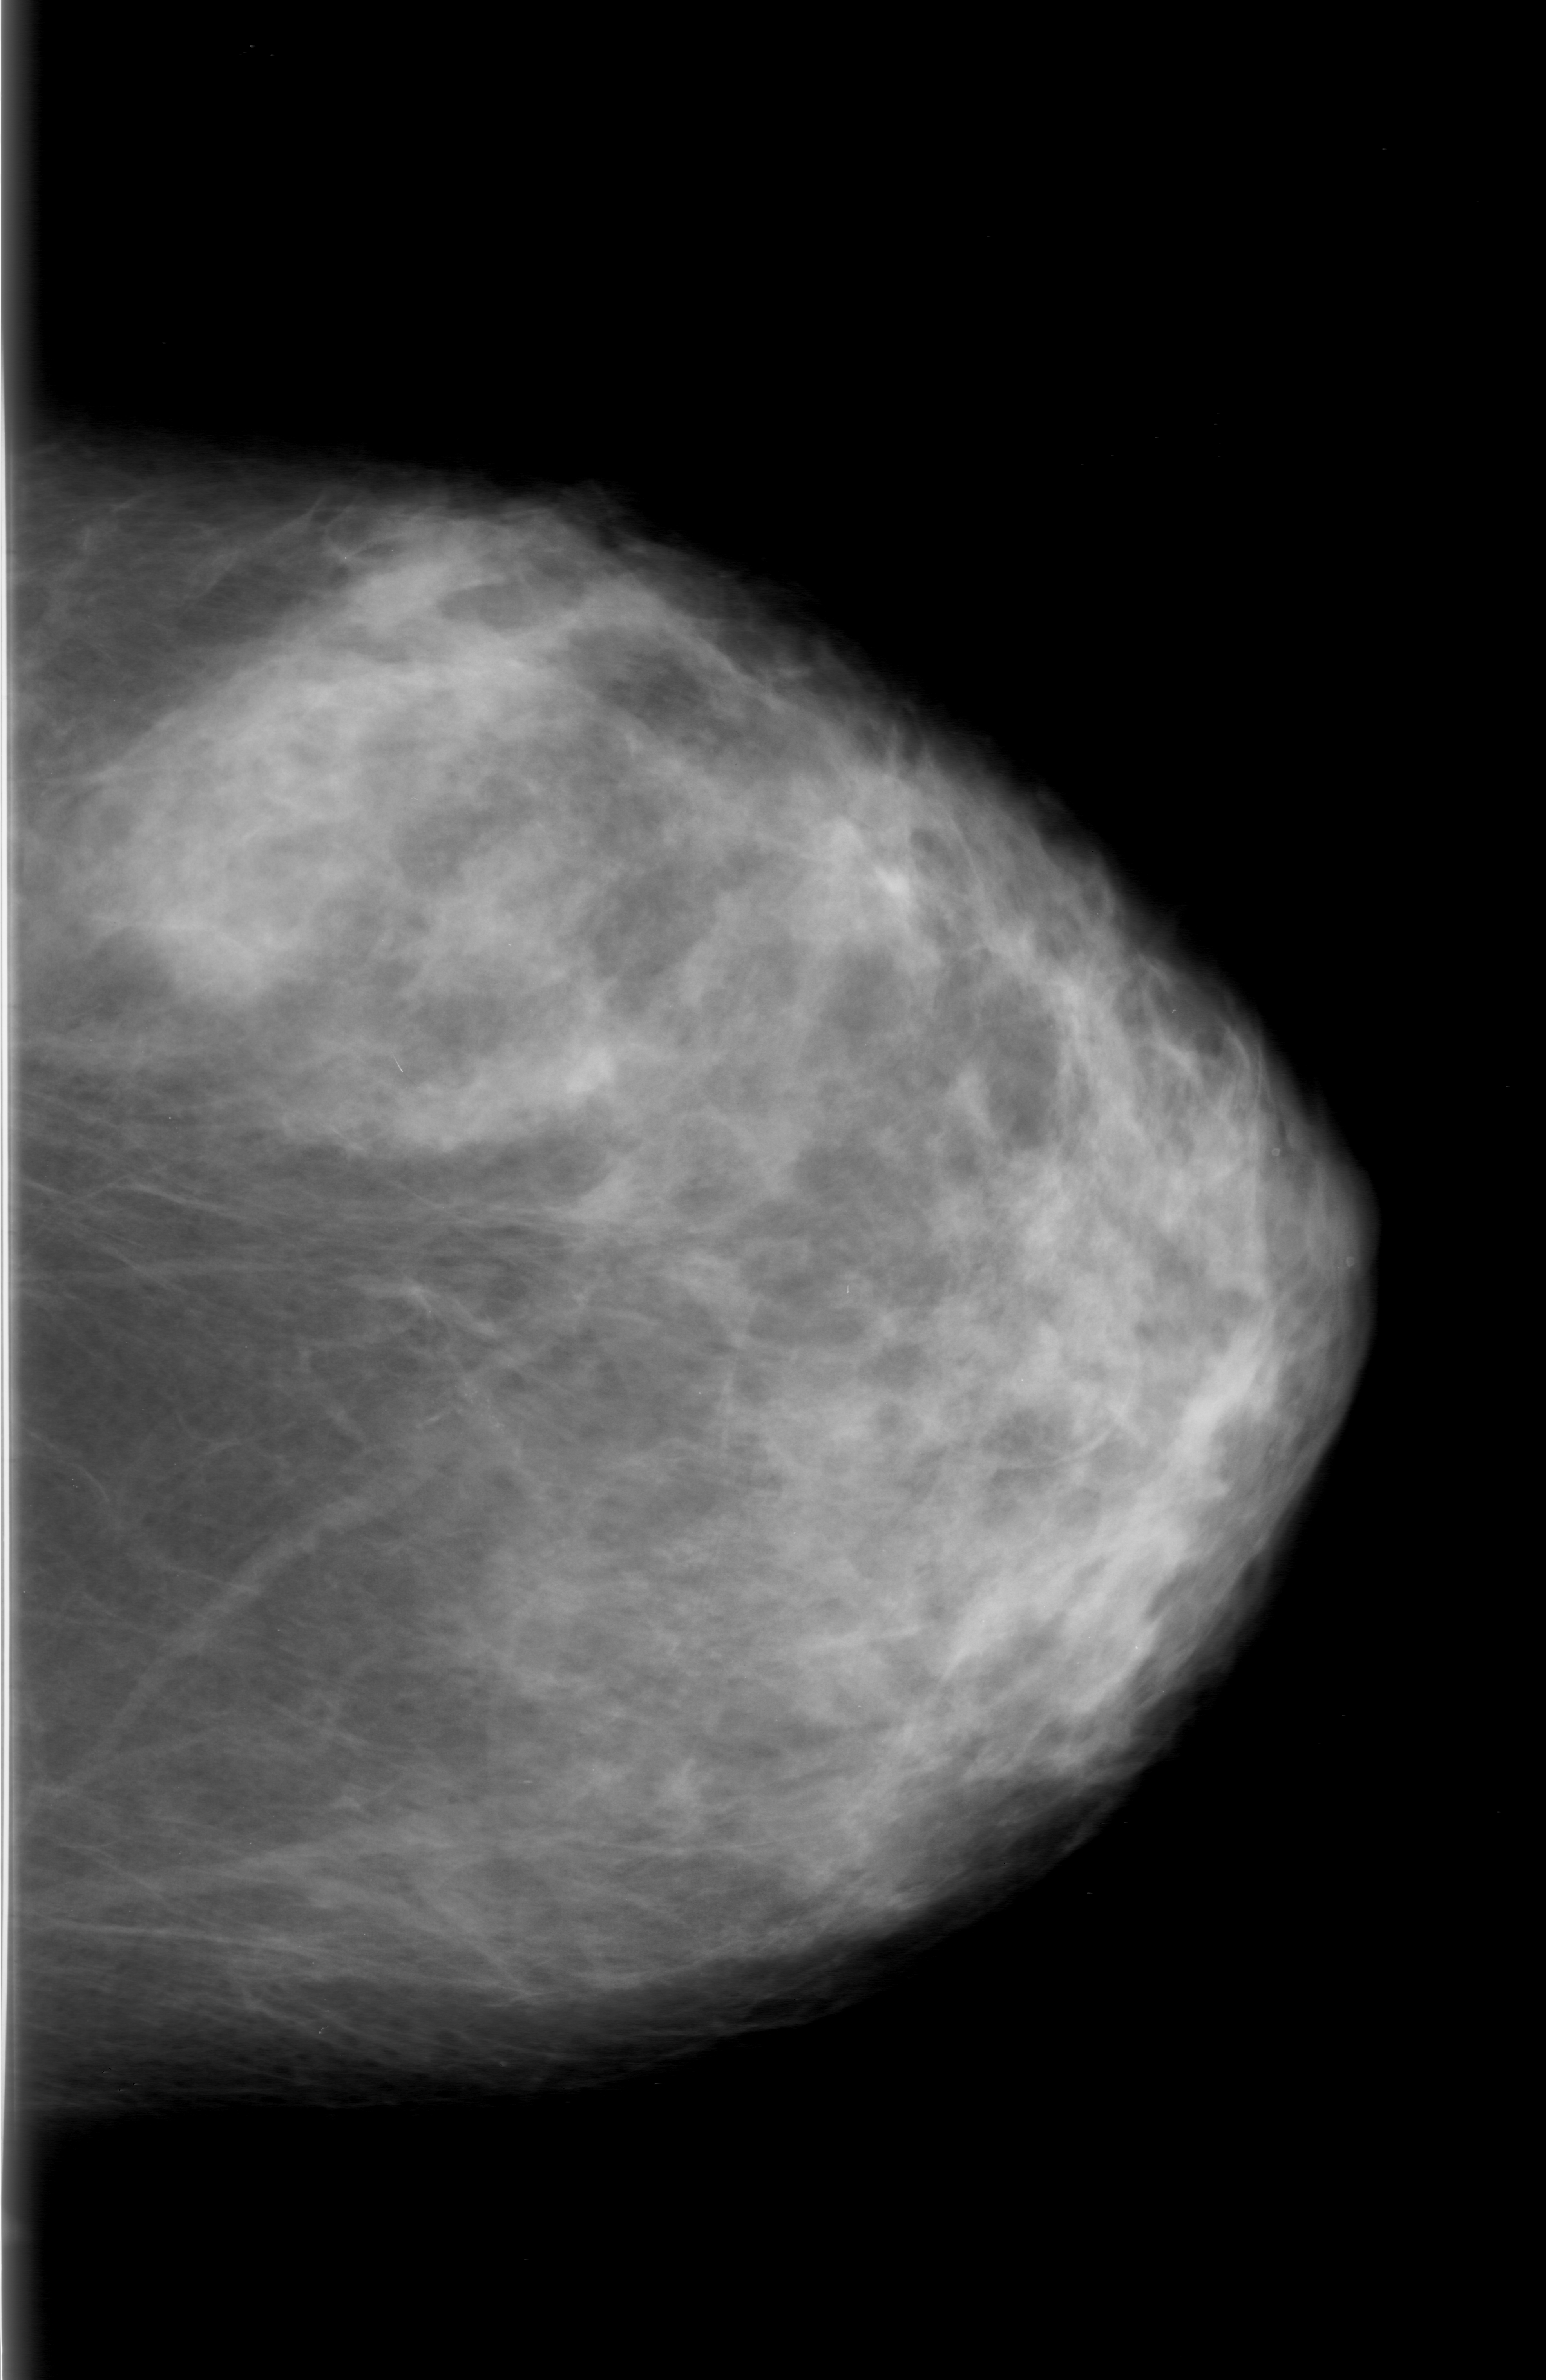
Digitized screen-film mammogram; left breast; CC view; BI-RADS breast density category 3 (scale 1–4); 1546 × 2380 image matrix.
Expert-marked regions of interest on this film, with their recorded descriptors:
- calcifications, morphology punctate / fine linear branching, distribution clustered; BI-RADS assessment category 0 (incomplete: needs additional imaging); pathology result (as recorded, not read from the image): malignant: bounding box [x1, y1, x2, y2] px = [383, 1332, 553, 1487]